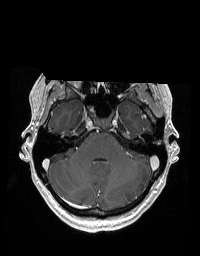
Brain MRI from a brain-tumour surgery series, one axial slice; slice 135 of 192 in the series (ordered by position); T1-weighted post-contrast; 1 mm slice thickness; 200 × 256 image matrix, field of view 195 × 250 mm. Case-level facts recorded for this patient, not image findings: histopathology: Glioblastoma; WHO grade: 2; IDH mutation: no; tumour location: Right Skull Base Temporal.
Outlined on this slice (outlined manually by an expert reader):
- tumour: bounding box [x1, y1, x2, y2] px = [76, 110, 83, 125]